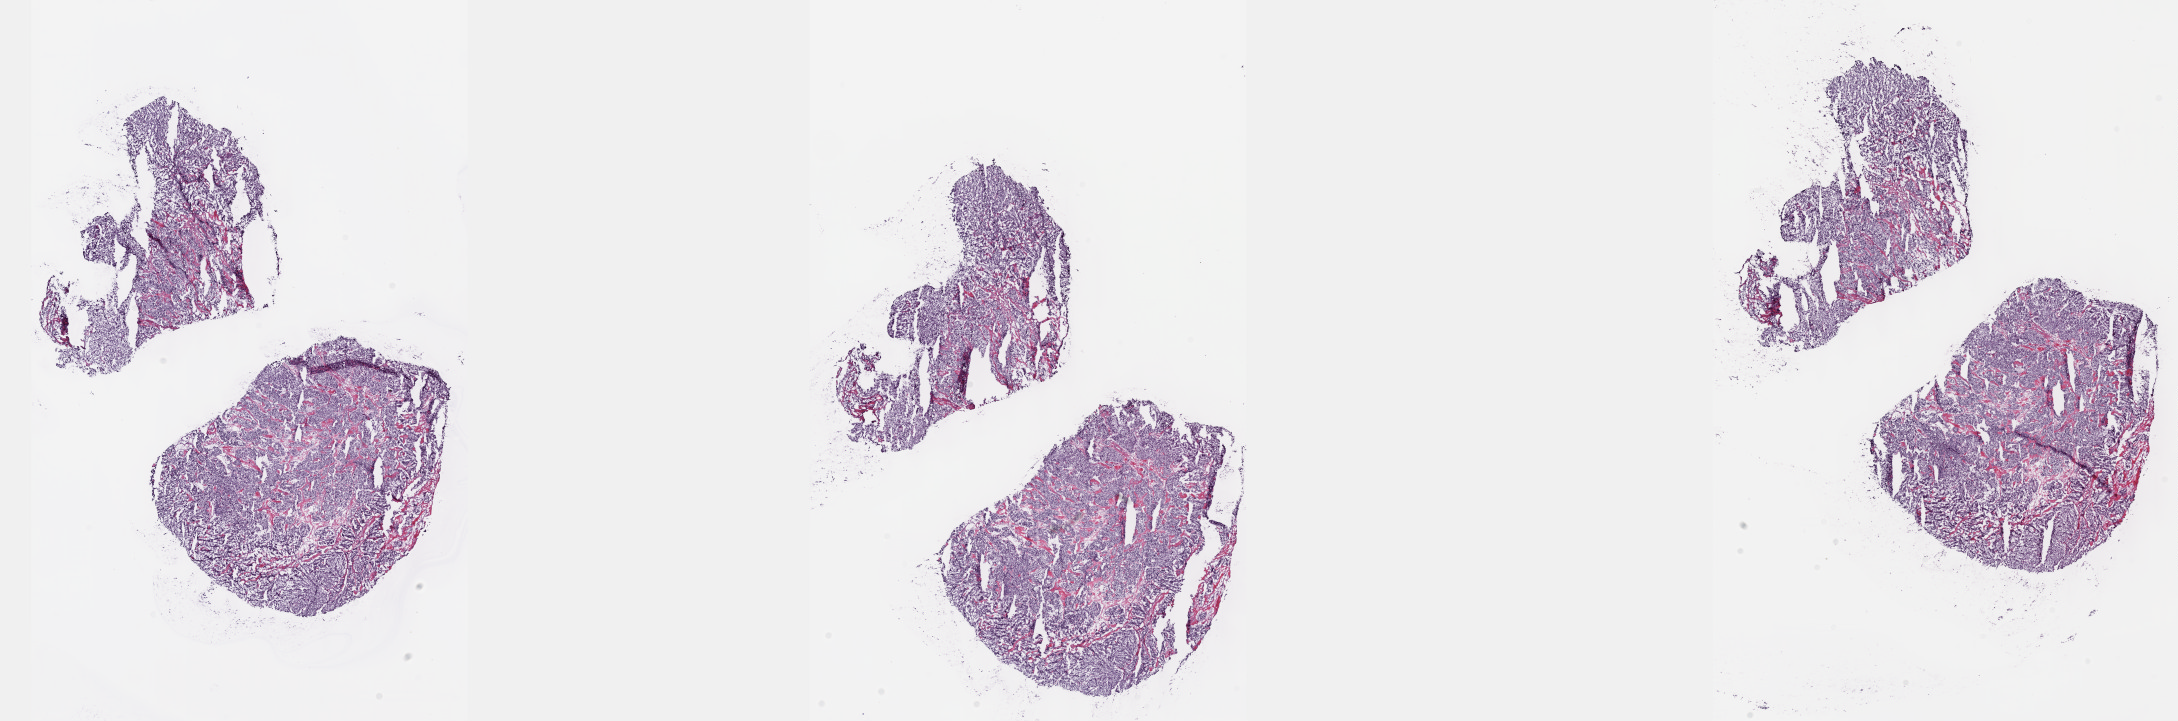
Digitized H&E tissue section (whole slide), low-resolution overview of the scanned area, about 35.2 x 11.7 mm (slide scanned at 40x), frozen section from the top of the tissue portion, adrenal gland, primary tumour sample. Patient: male, age at initial diagnosis 40 years. Composition of this section per pathologist review: tumour cells 100%, tumour nuclei 75%, normal cells 0%, stromal cells 0%, necrosis 0%. Inflammatory infiltration, as recorded: lymphocyte infiltration 1%, monocyte infiltration 0%, neutrophil infiltration 0%.
Laterality: right. Diagnosis: Pheochromocytoma, NOS.